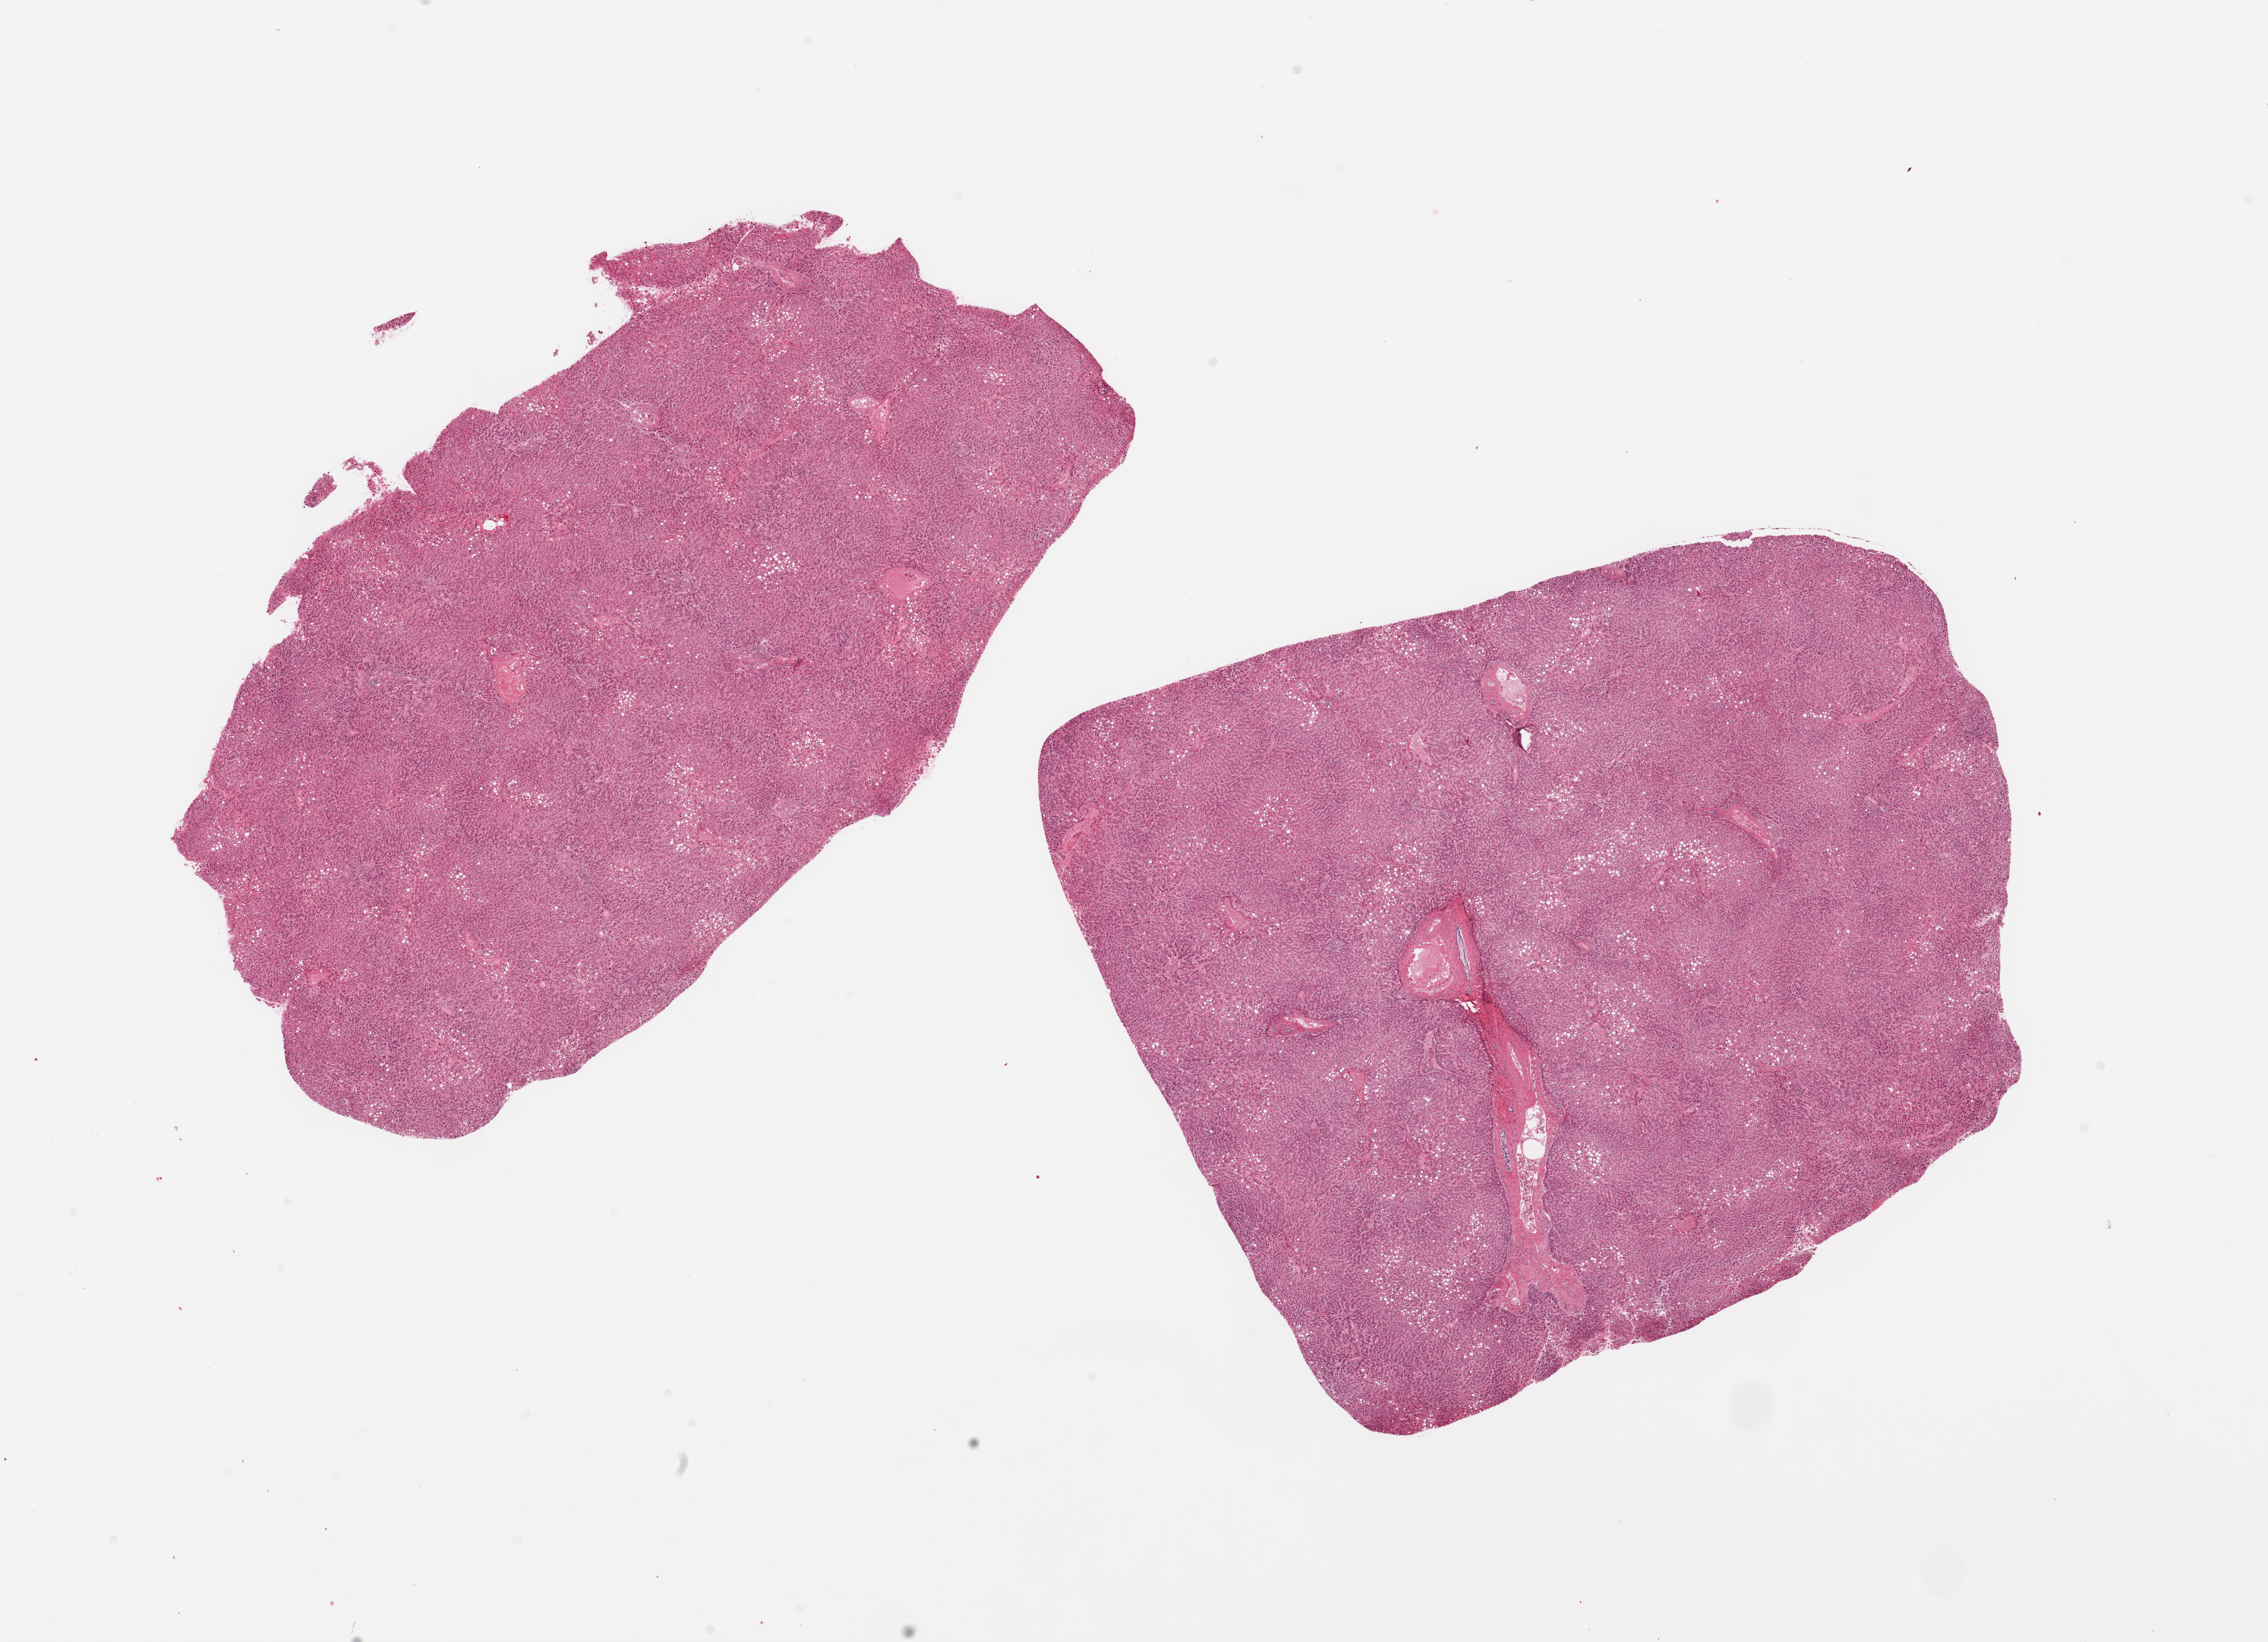
Haematoxylin and eosin whole-slide image, whole scanned area (about 23.6 x 17.1 mm, acquisition: 20x scan) shown as a low-resolution overview; PAXgene-fixed paraffin-embedded (PFPE) section; target tissue: liver; tissue donor sample.
Review note (as recorded): 2 pieces, moderate congestion, macrovesicular steatosisinvolves 20-30 % of parenchyma.